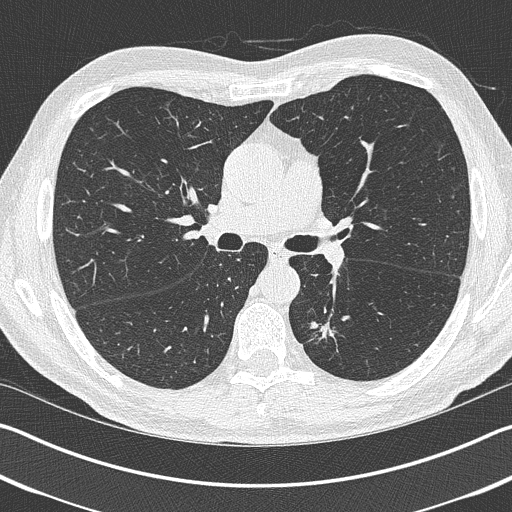
Low-dose screening chest CT, one axial slice; slice 247 of 402 in the series (ordered by position); reconstruction kernel B50f; lung window (W 1500 / L -600 HU); 1 mm slice thickness; 512 × 512 image matrix, field of view 340 × 340 mm.
Annotated regions visible in this slice (outlined manually by an expert reader):
- lesion 1 (tumor, lower lobe of left lung): bounding box <311,322,334,339> (left, top, right, bottom; pixels)